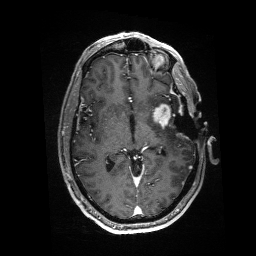
Brain MRI from a brain-tumour surgery series, one axial slice. Position 90 of 176 along the scan axis. T1-weighted post-contrast. 256 × 256 image matrix, field of view 256 × 256 mm. Case-level facts recorded for this patient, not image findings: histopathology: Glioblastoma; WHO grade: 4; IDH mutation: no; tumour location: Left Anterior/Superior Temporal.
Structures marked on this image (expert manual segmentation):
- residual tumour: bounding box (x1, y1, x2, y2) in pixels: (153, 103, 183, 128)